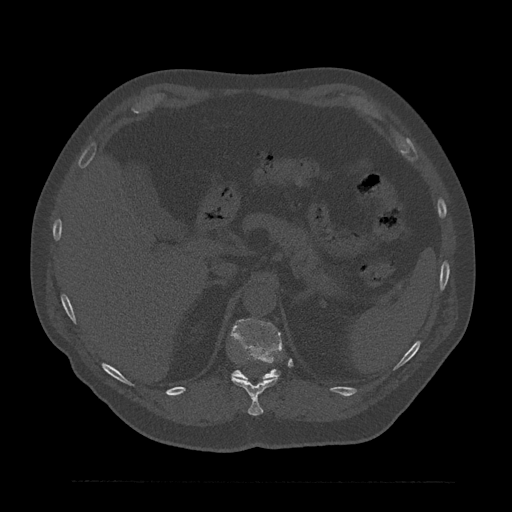
CT including the spine, one axial slice. Position 264 of 797 along the scan axis. Reconstruction kernel Br40s/3. 120 kVp. Bone window (W 1800 / L 400 HU). 0.5 mm slice thickness. 512 × 512 image matrix. Male patient, age 61 years. From the clinical record (not read from this slice): primary cancer: prostate.
Structures marked on this image (semi-automatically segmented with operator editing):
- T11 vertebra: bounding box [x1, y1, x2, y2] px = [231, 375, 279, 416]
- T12 vertebra: [231, 319, 282, 381]